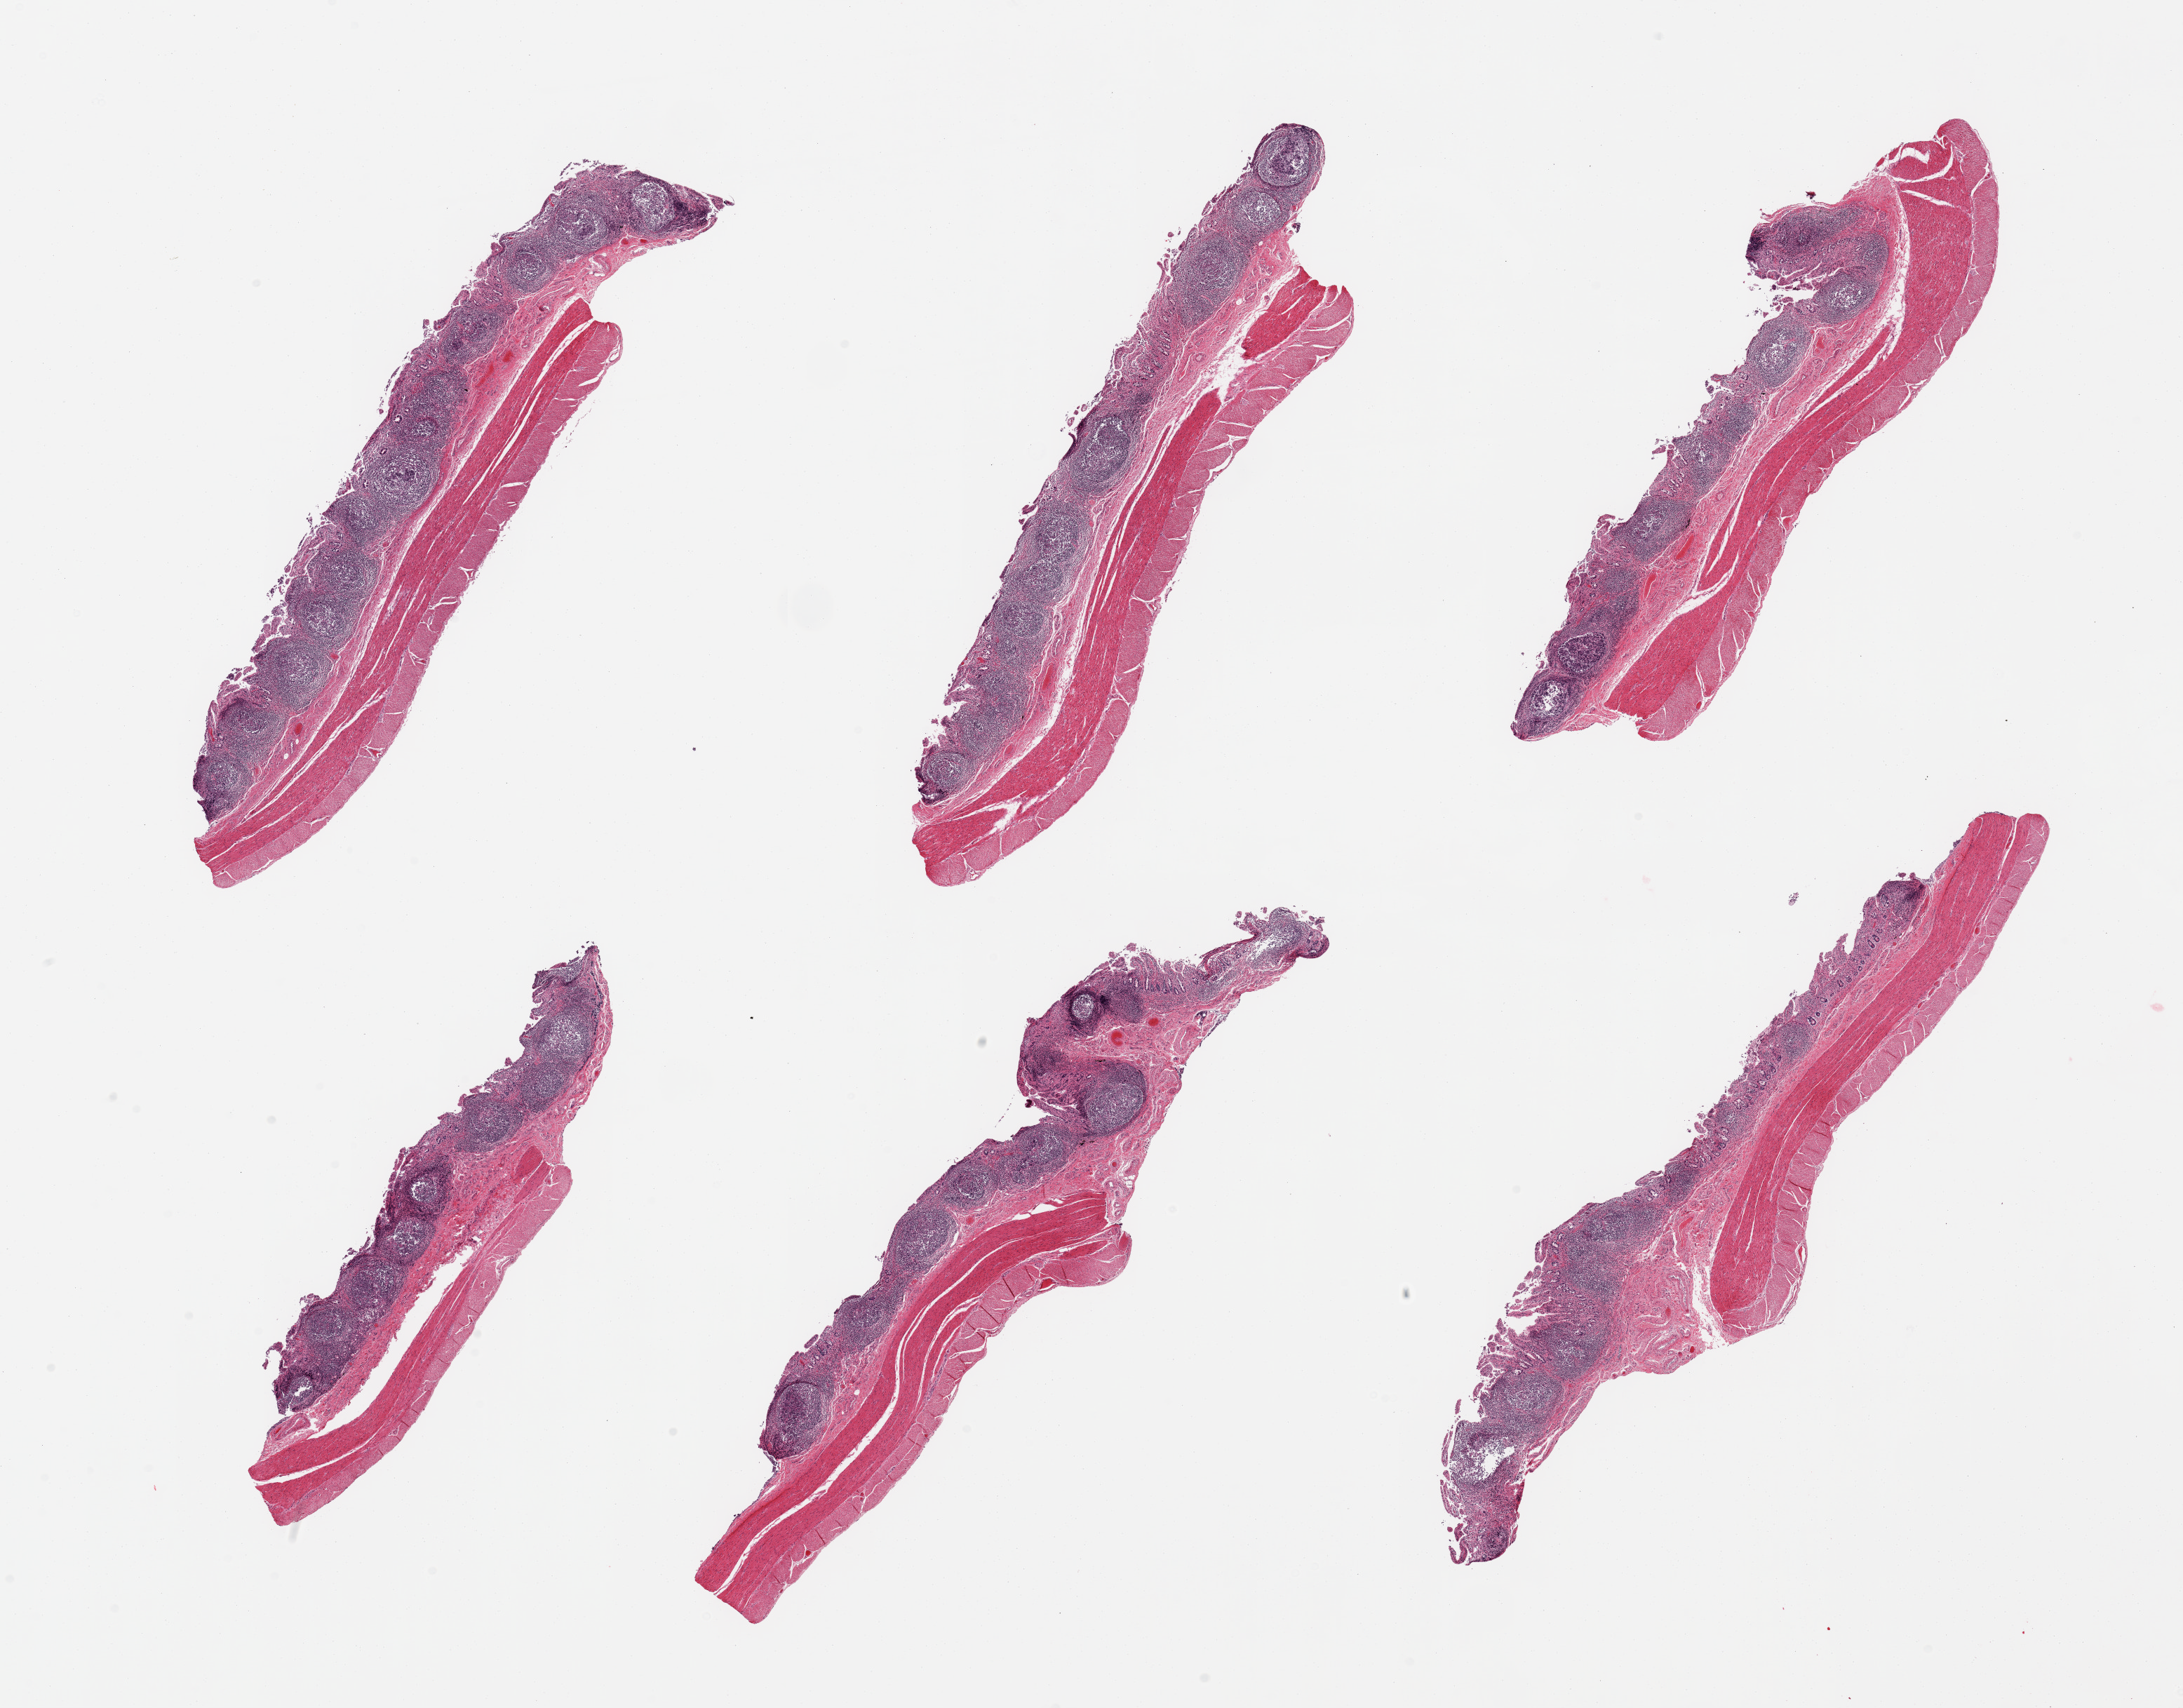
H&E whole-slide image, shown as a low-resolution overview of the whole scanned area (about 24.6 x 19.3 mm); PAXgene-fixed, paraffin-embedded tissue; sampled site (target tissue): transverse colon; donor tissue sample. Donor: male.
Pathologist's review note for this sample: 6 pieces, glandular epithelium totally auotlyzed.